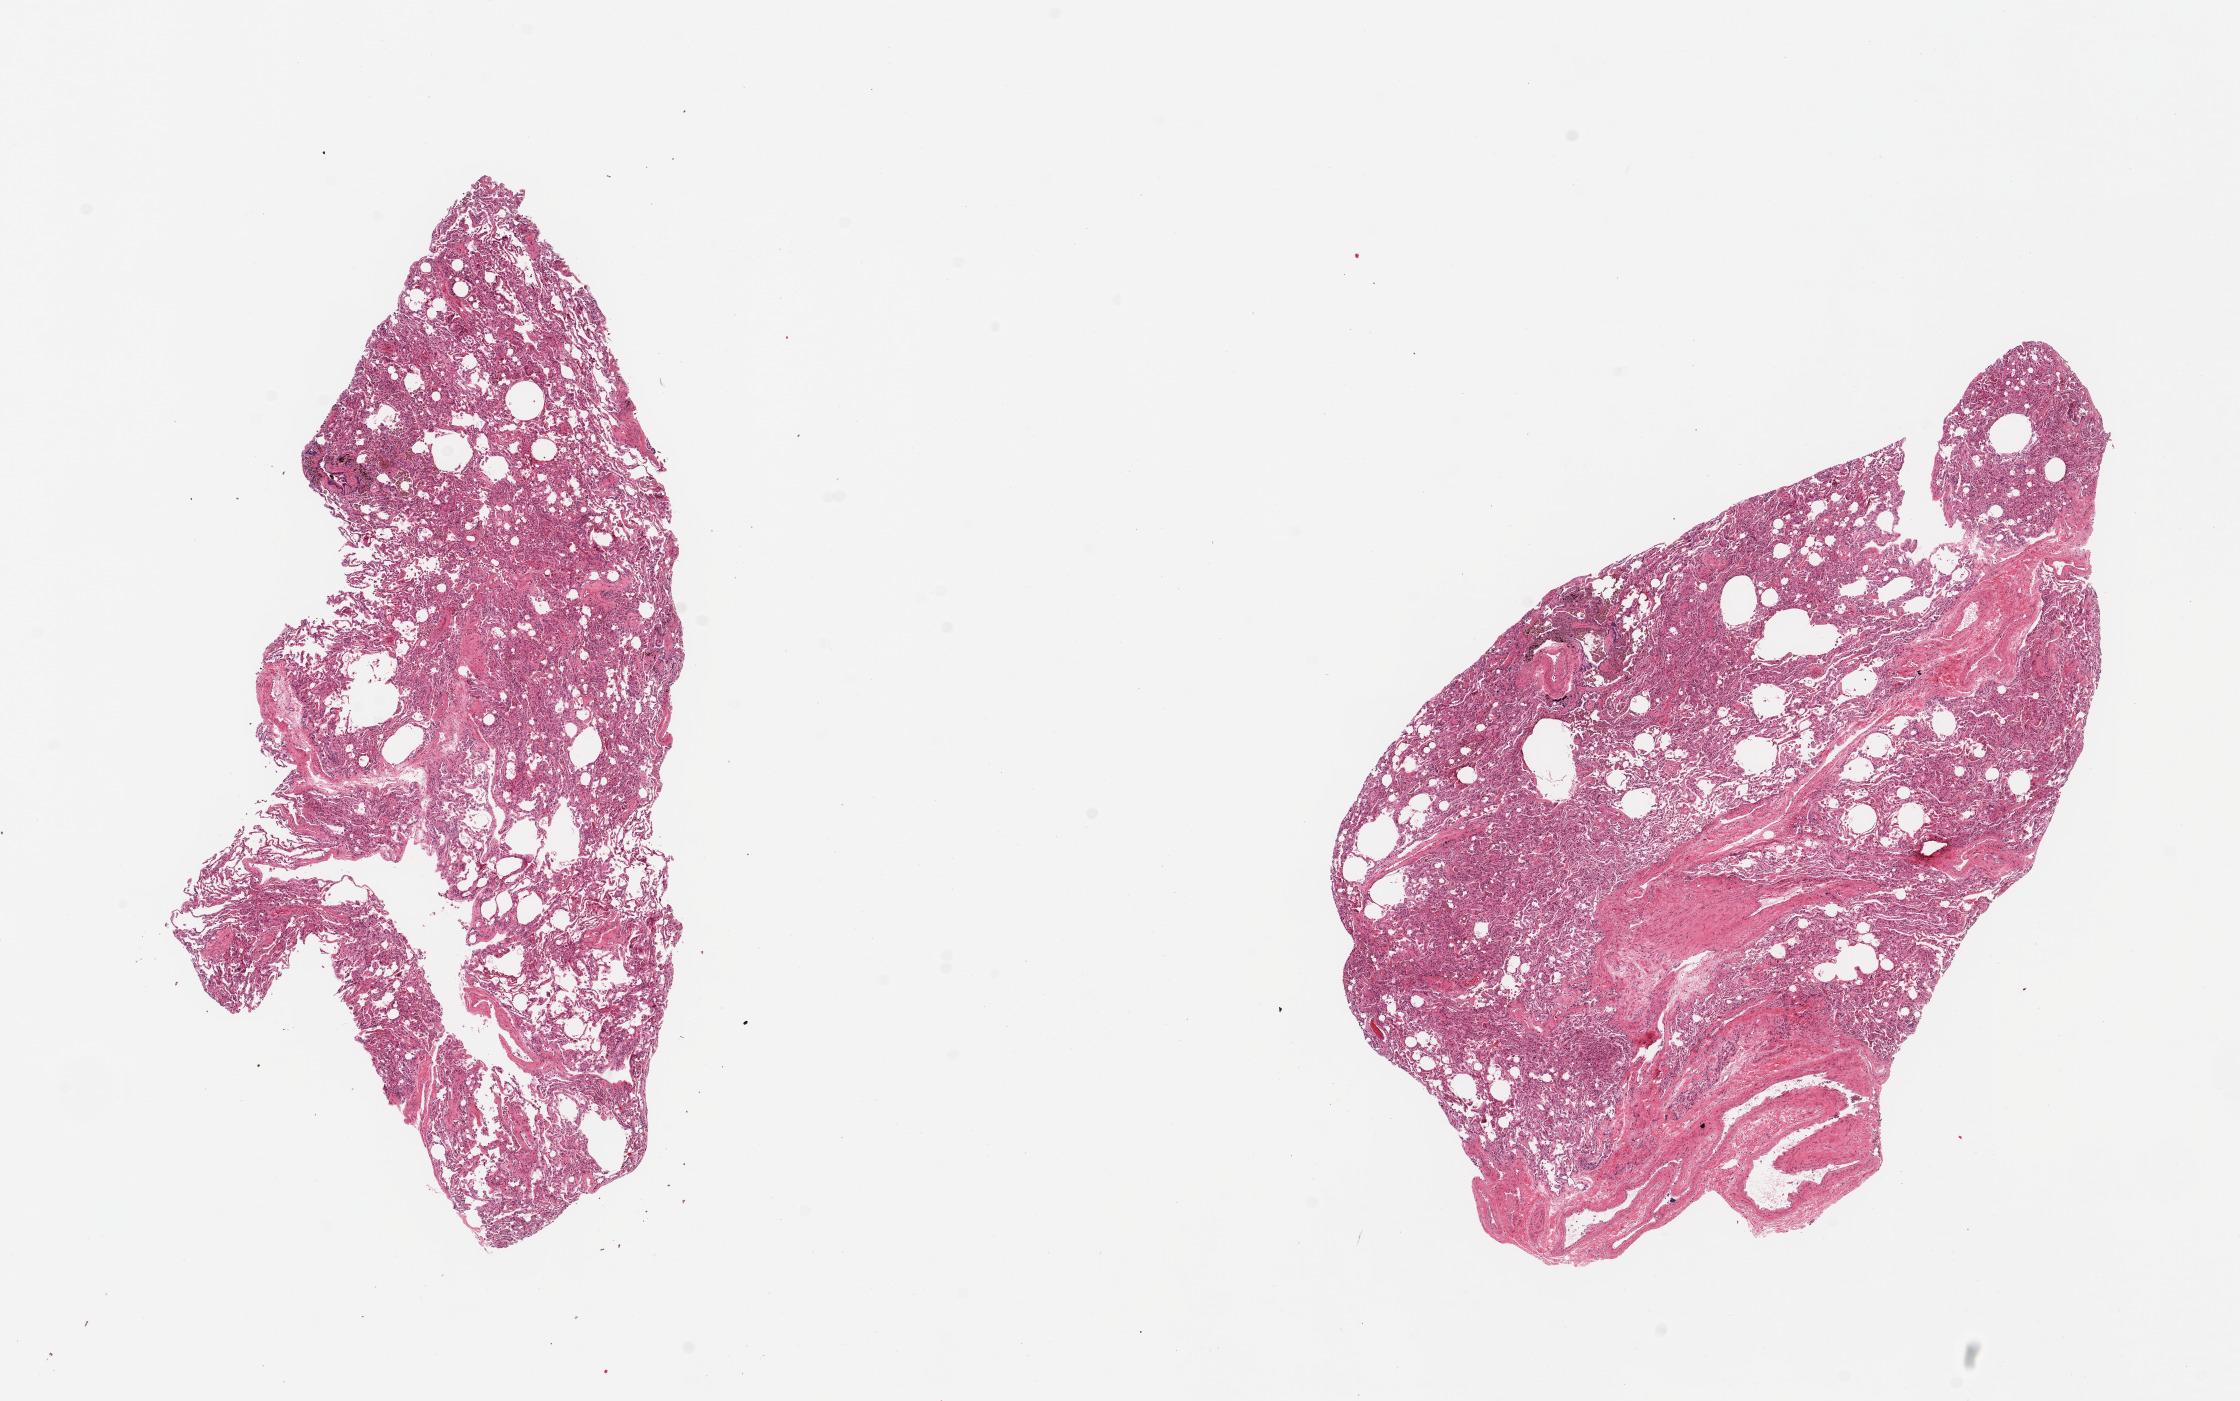
Hematoxylin and eosin (H&E) whole-slide image, brightfield, whole scanned area (about 17.7 x 11.1 mm, from a 20x scan) shown as a low-resolution overview, PAXgene-fixed paraffin-embedded (PFPE) section, target tissue: lung, tissue donor sample. Donor sex: male.
Review note (as recorded): 2 pieces; moderate number of pigmented alveolar macrophages; 2 large veins in 1 piece.